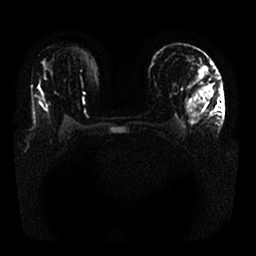
Breast MRI, one axial slice; slice 17 of 25 in the series (ordered by position); diffusion-weighted series; image 2 of 4 stored at this slice position (different b-values; order by instance number); 1.5 T; 4 mm slice thickness; 256 × 256 image matrix, field of view 340 × 340 mm. Female patient.
Outlined on this slice (outlined manually by an expert reader):
- tumour on diffusion-weighted imaging: bounding box [x1, y1, x2, y2] px = [189, 86, 212, 124]